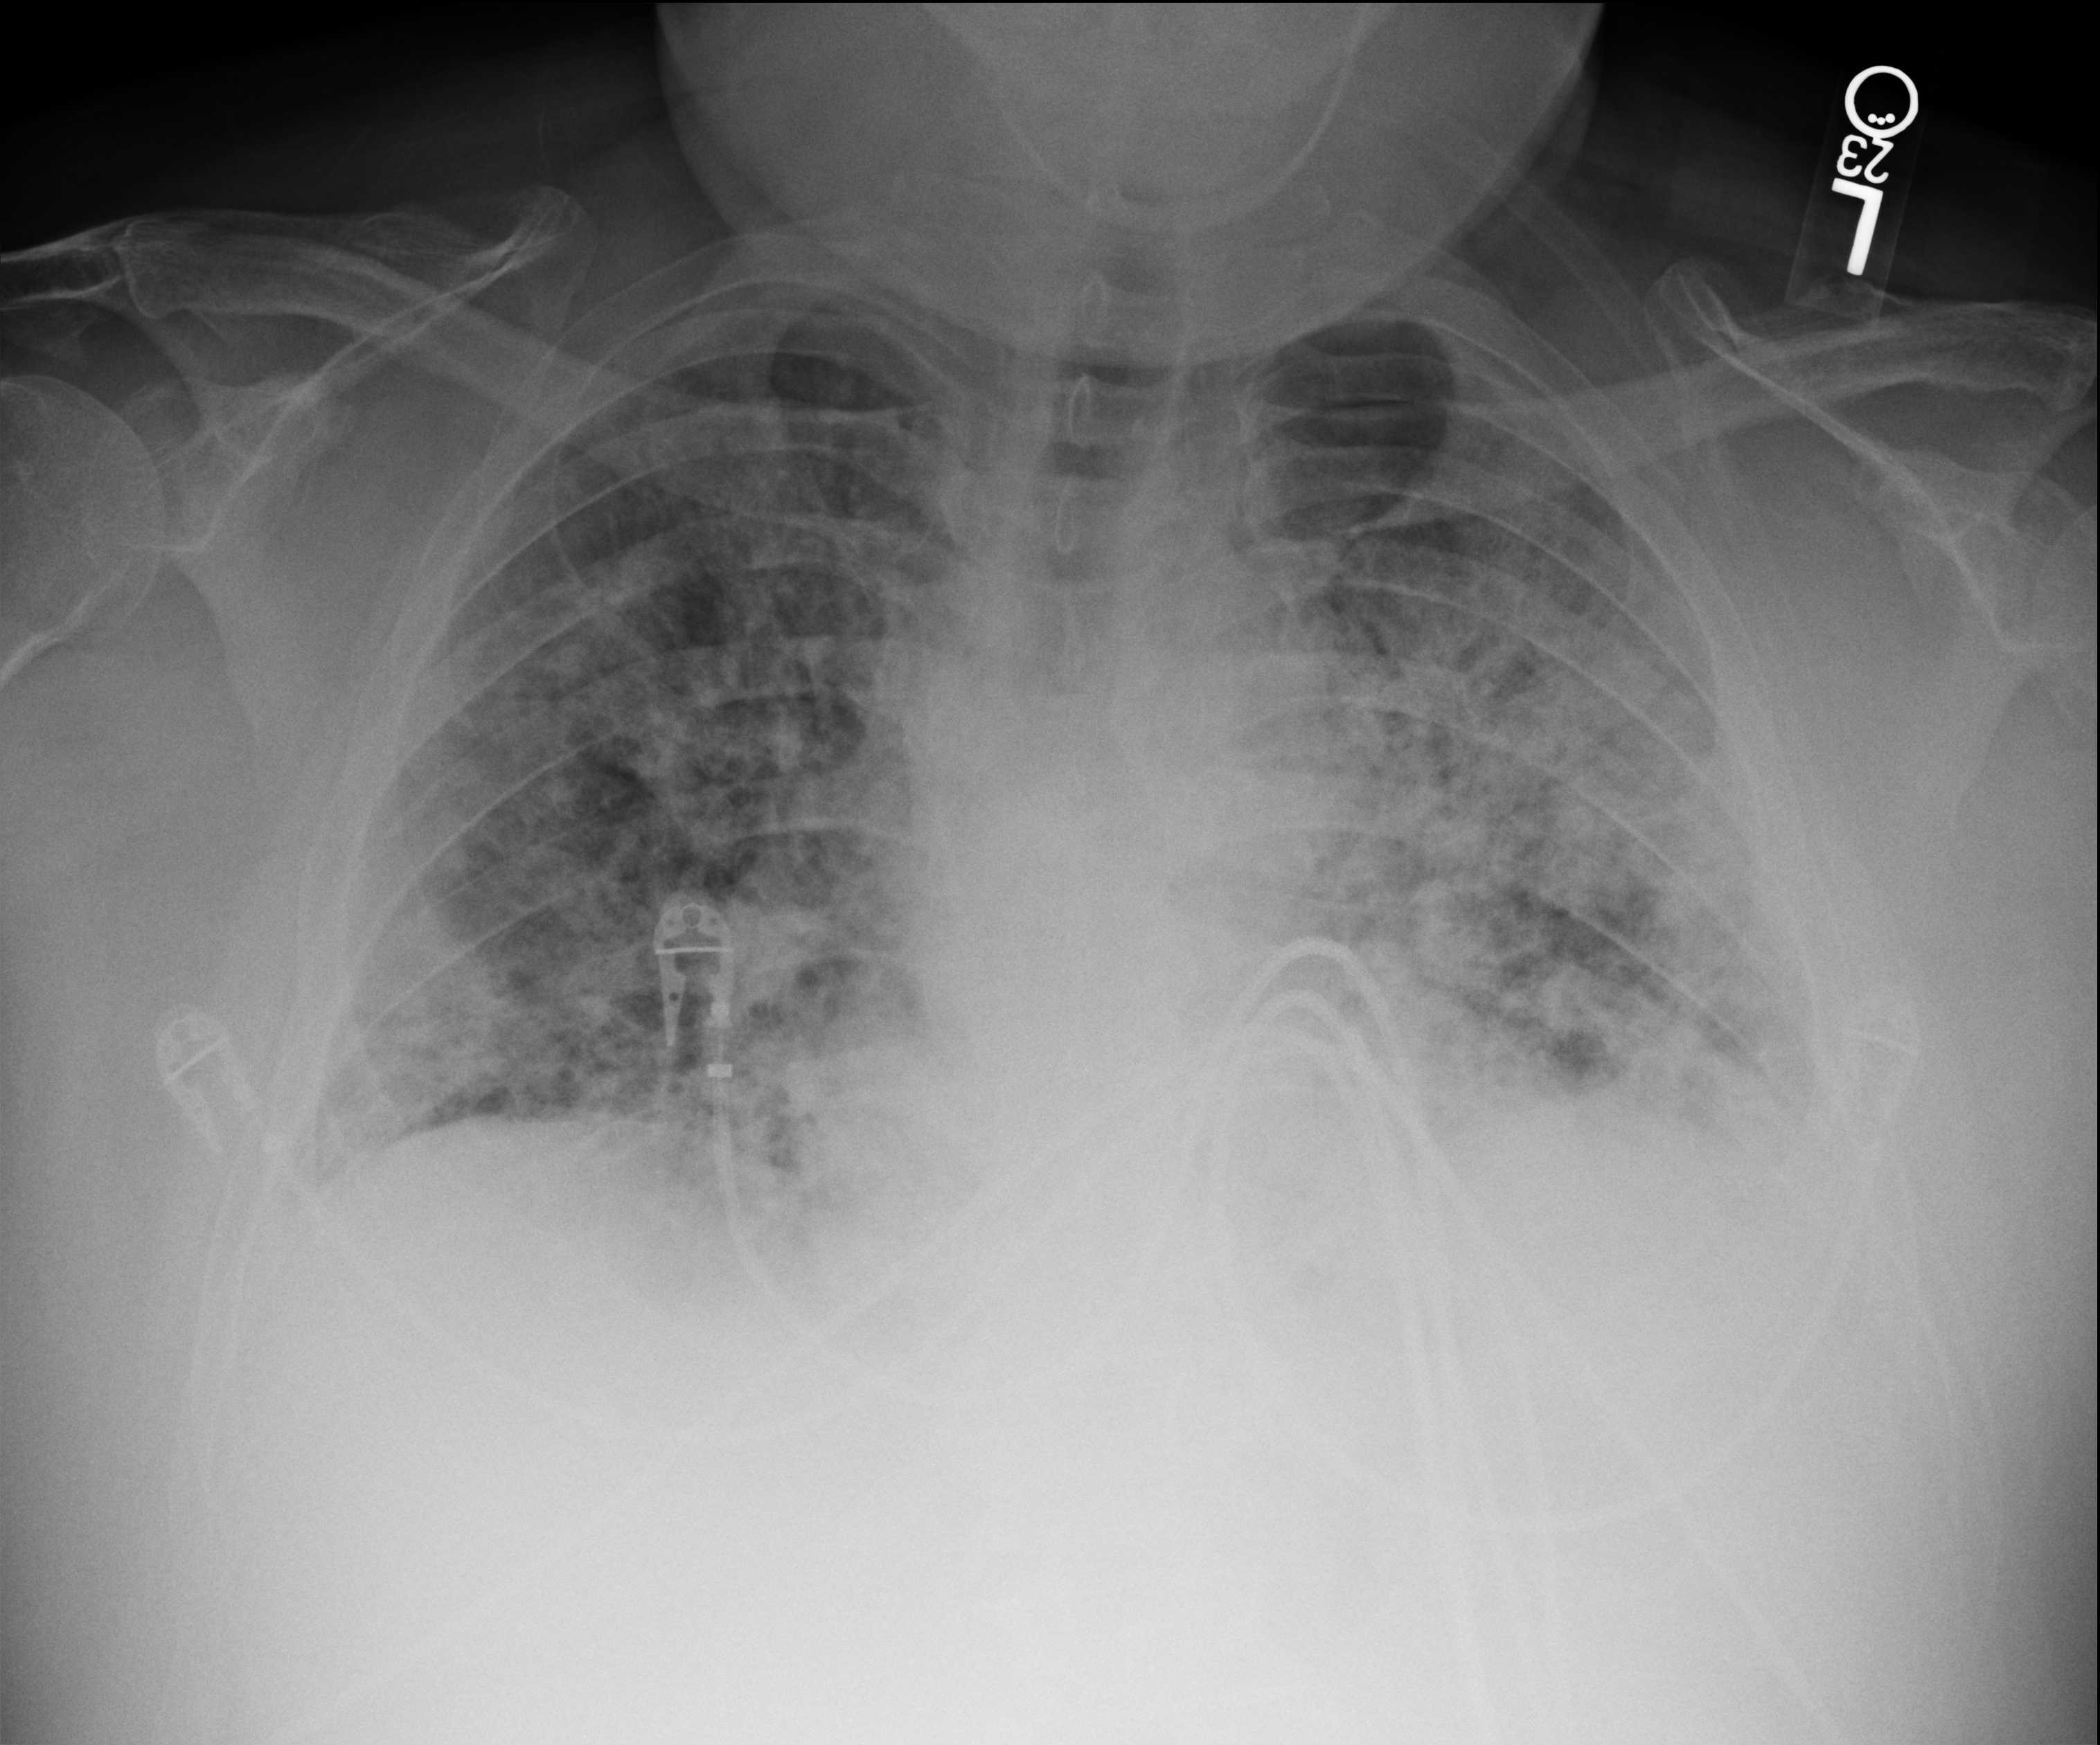
Bedside chest radiograph (computed radiography). Patient hospitalised with COVID-19; male, aged 18–59 years.
From the hospital-stay record, not from the radiograph (when in the stay this image was taken is not recorded): mechanically ventilated during this hospital stay: no; admitted to intensive care during this hospital stay: no; diabetes (admission record): yes.